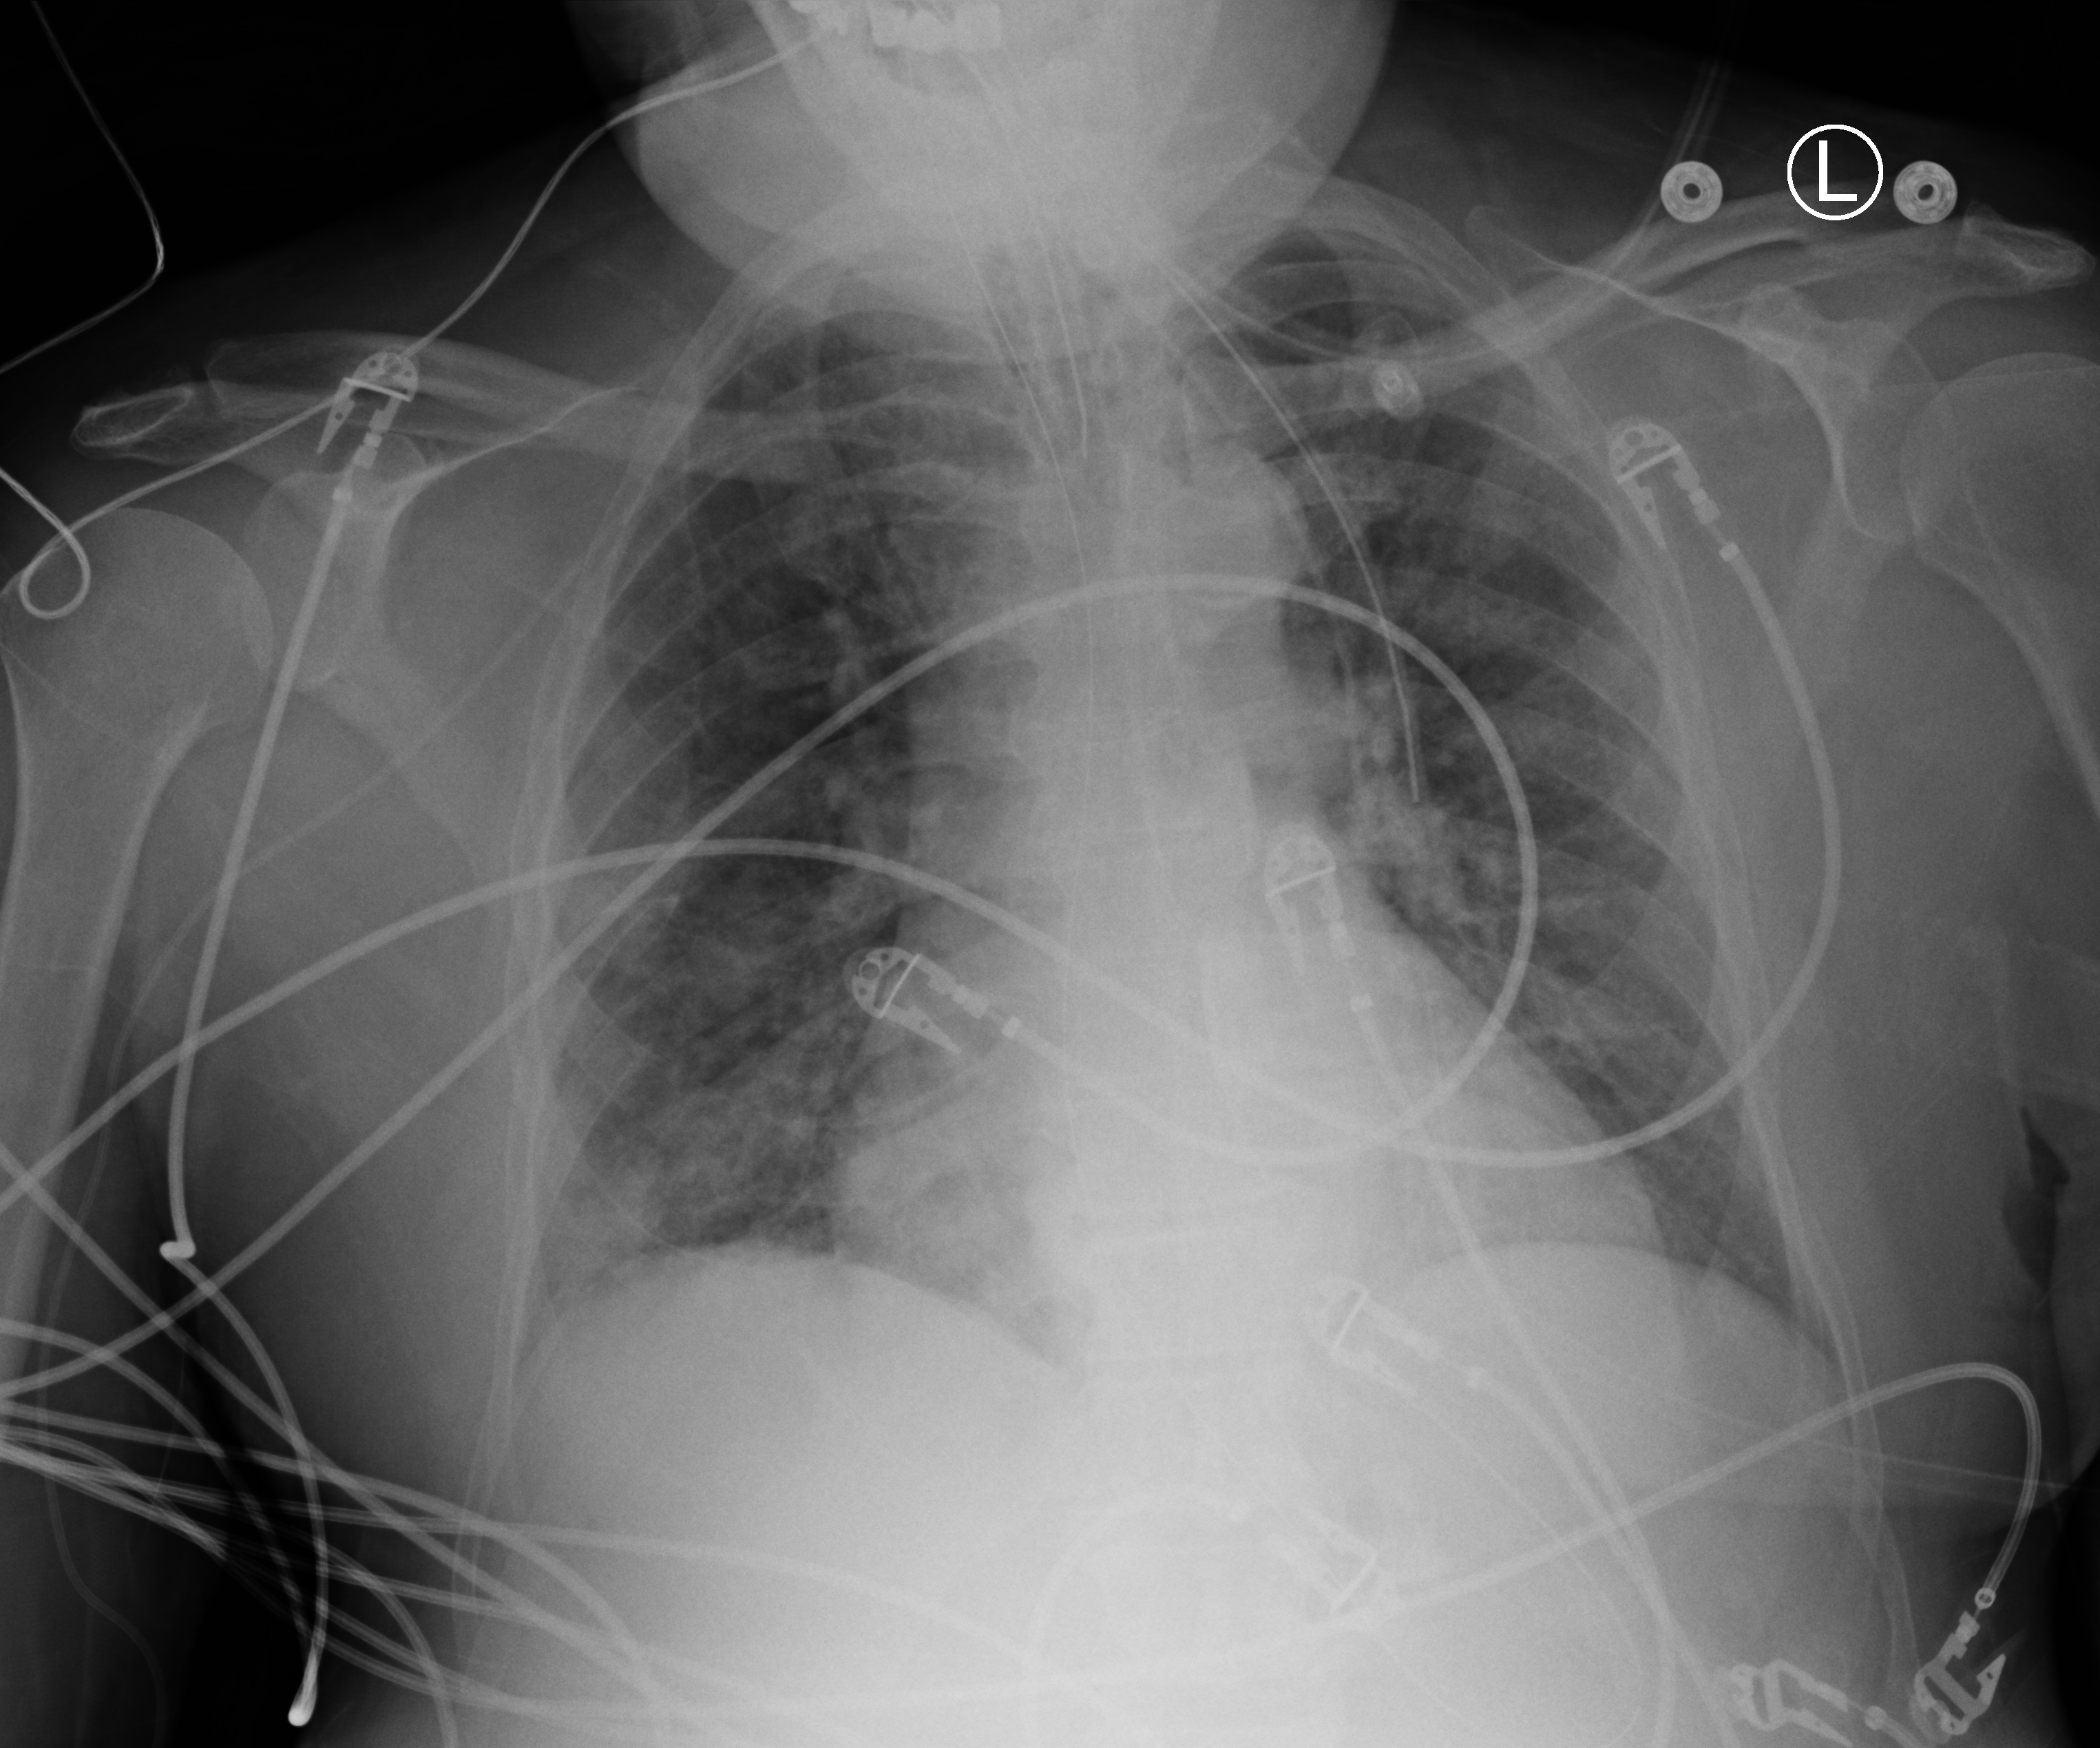
Portable chest radiograph, anteroposterior (AP) projection. Male patient hospitalised with COVID-19, age 60–74 years.
Admission-level facts for this patient (not findings on this image; timing relative to this image not recorded):
- hypertension (admission record): yes
- admitted to intensive care during this hospital stay: yes
- mechanically ventilated during this hospital stay: yes